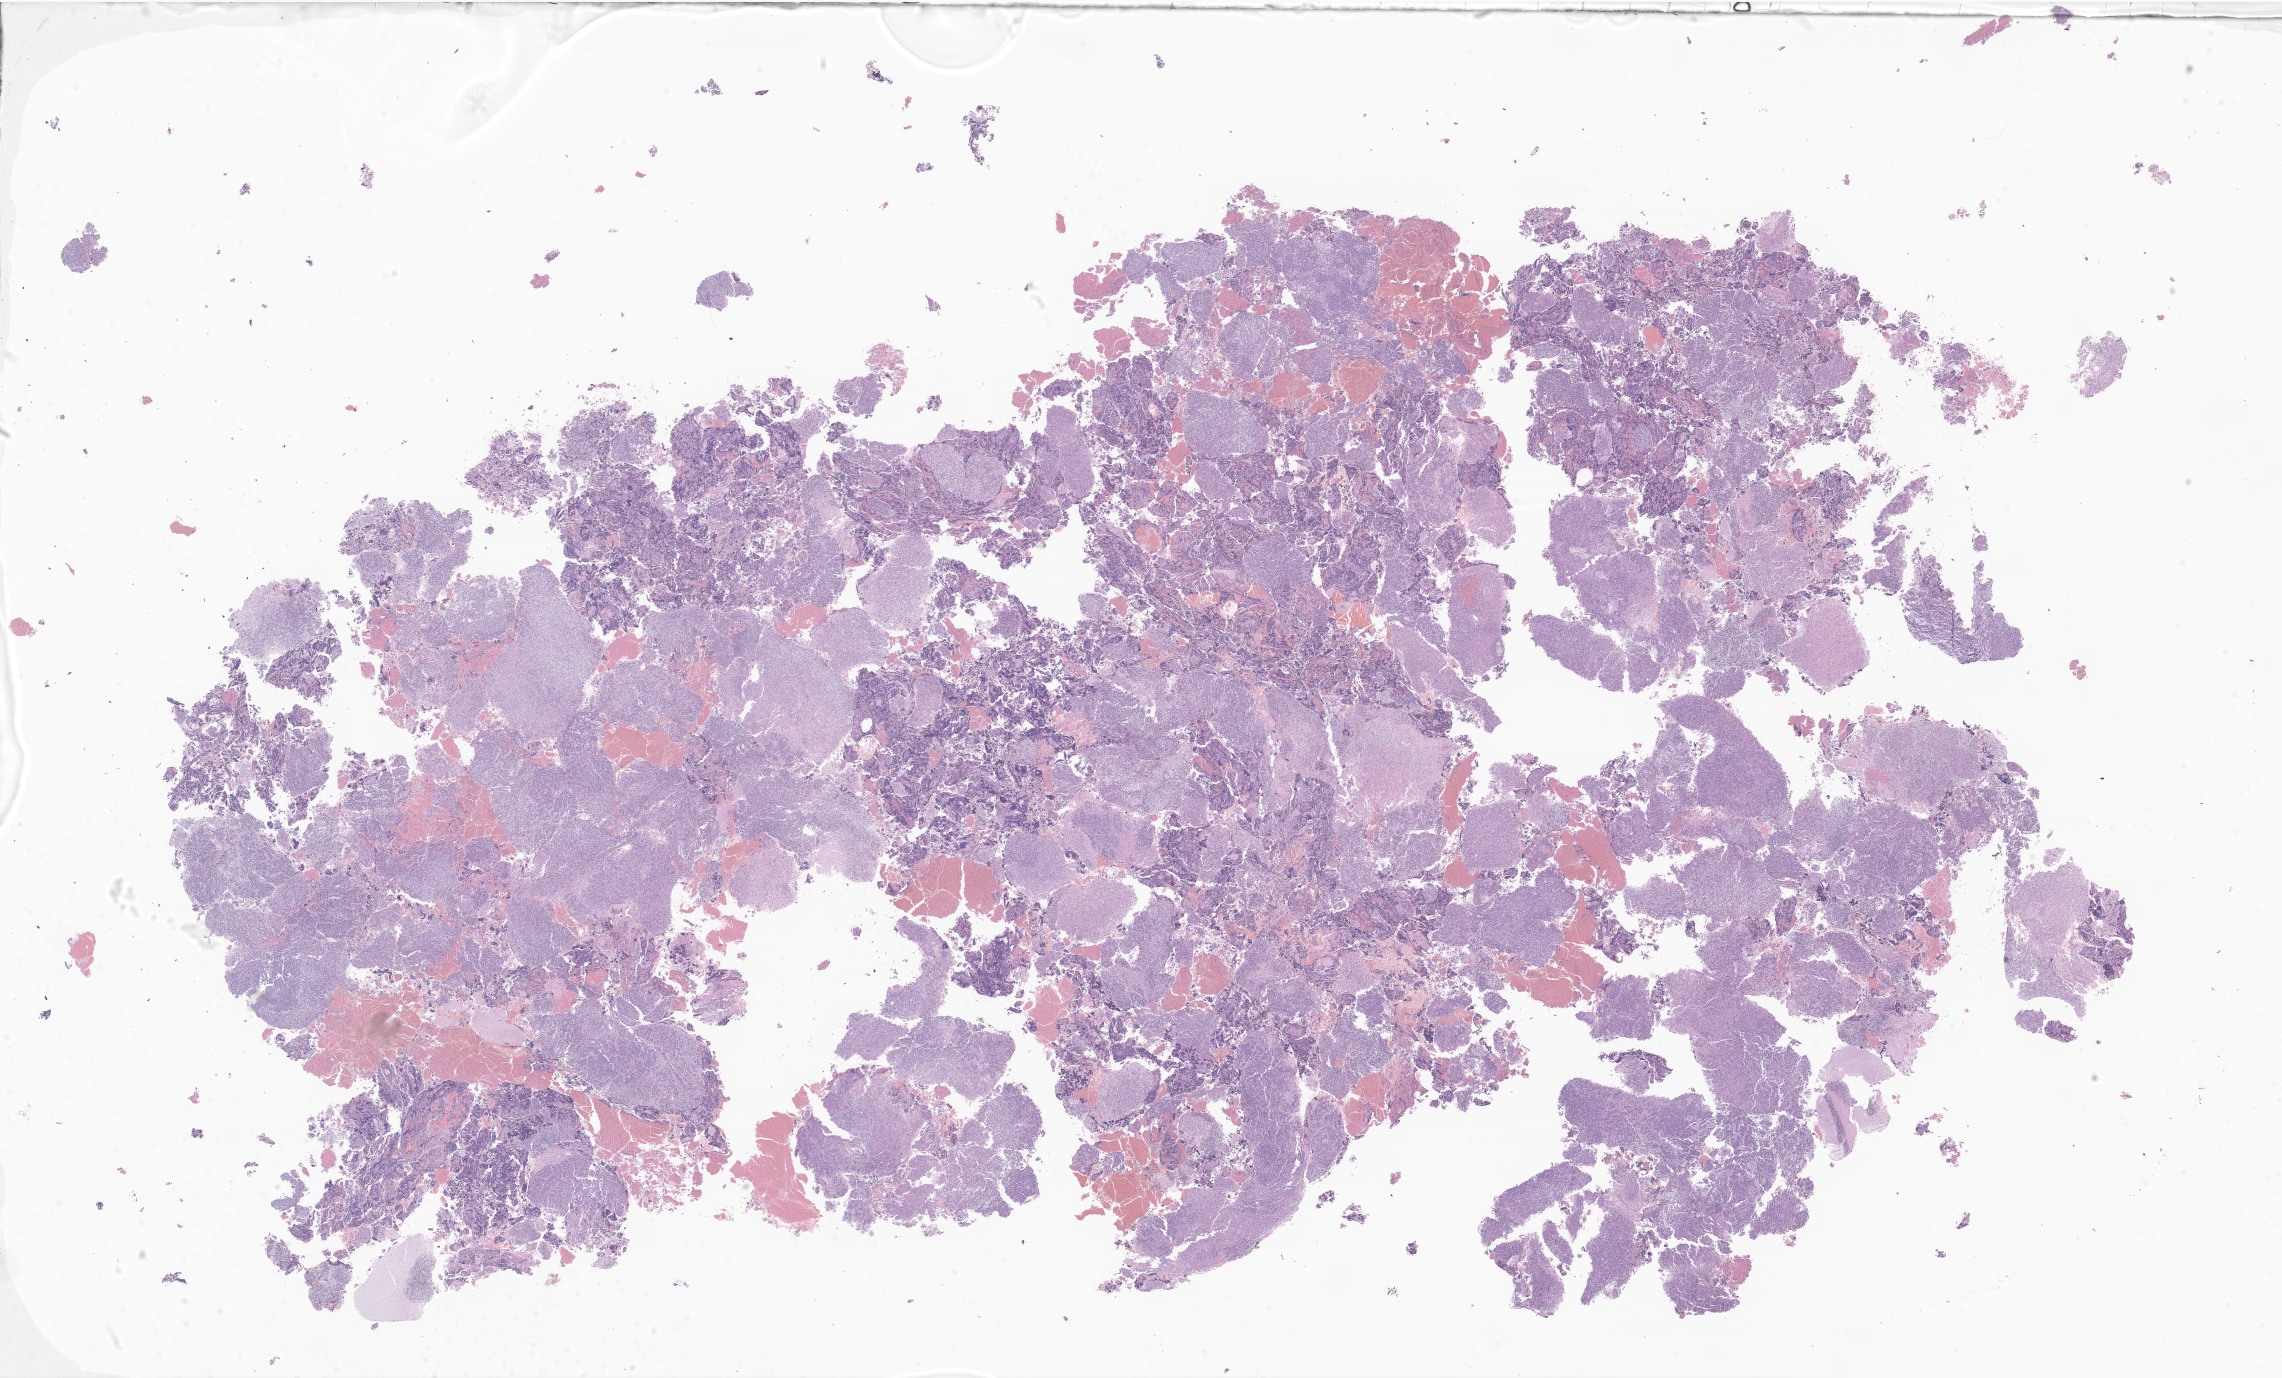
Whole-slide image, haematoxylin and eosin stain of tumor tissue from the brain, a low-resolution overview of the entire scanned area, about 38.5 x 23.2 mm; formalin-fixed paraffin-embedded section. Patient: female, age 91 months (7 years 7 months).
Recorded diagnosis: Medulloblastoma, NOS.